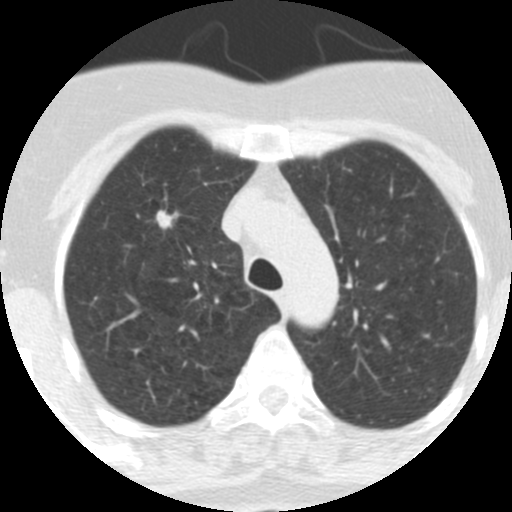
Chest CT (low-dose screening protocol), one axial image, first (baseline) screen, lung window (W 1500 / L -600 HU), 2.5 mm slice thickness, standard (soft-tissue) reconstruction kernel (STANDARD), 120 kVp. Female participant, aged 62 years at enrolment. Current smoker at enrolment.
Lesion marked by an expert reader, bounding box (x1, y1, x2, y2) in pixels: (116, 162, 183, 234). The exam's reader record, not a measurement of the box and not confirmed to be the same lesion: non-calcified nodule or mass ≥4 mm, right upper lobe, 9 × 7 mm, spiculated (stellate) margins, soft tissue attenuation. Official screen result: positive, change unspecified: nodule(s) >= 4 mm or enlarging nodule(s), mass(es), or other non-specific abnormalities suspicious for lung cancer. Later outcome: lung cancer diagnosed 126 days after this screen — adenocarcinoma, NOS, right upper lobe, moderately differentiated (G2), stage IA (AJCC 6th edition), 18 mm at pathology.